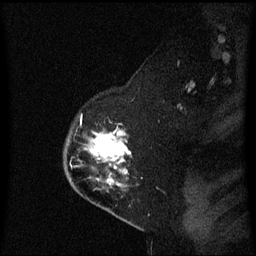
Breast MRI (dynamic contrast-enhanced), one sagittal slice. Dynamic contrast-enhanced series, image 2 of 3 at this slice position (ordered by acquisition). 1.5 T. TE 4.2 ms, TR 8.4 ms. 2 mm slice thickness. 256 × 256 image matrix, field of view 210 × 210 mm. Female patient, age 54 years. From the clinical record (not read from this slice): setting: breast cancer imaged before/during neoadjuvant chemotherapy; receptor status: HER2-positive.
Structures marked on this image (semi-automatically segmented with operator editing):
- analysis volume of interest (the breast-tissue region the enhancement analysis was run in; not a lesion): box from (x=66, y=133) to (x=133, y=198) px
- tumour enhancement mask (voxels above the 70 % enhancement threshold inside the analysis volume of interest): (x=93, y=135)–(x=127, y=183)